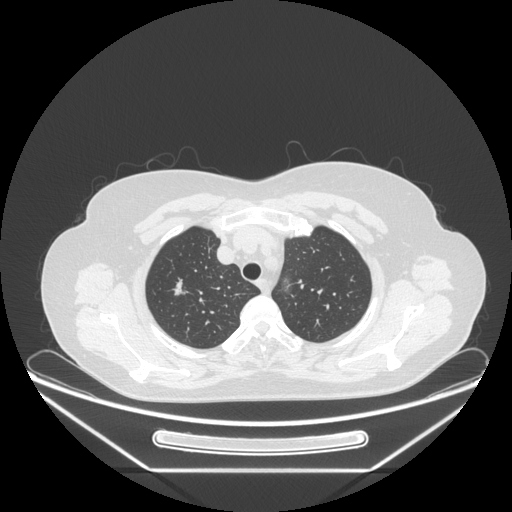
Chest CT, one axial slice. Slice 200 of 236 in the series (ordered by position). Reconstruction kernel STANDARD. 120 kVp. Lung window (W 1500 / L -600 HU). 1.25 mm slice thickness. 512 × 512 image matrix, field of view 433 × 433 mm. Patient: female, 60 years. Case-level facts recorded for this patient, not image findings: clinical TNM (as recorded): T1c N0 M0; histopathological grade: G2-3.
Structures marked on this image (rectangle marked by the reading radiologist):
- lung tumour (recorded histology: adenocarcinoma): bounding box (x1, y1, x2, y2) in pixels: (163, 264, 184, 304)